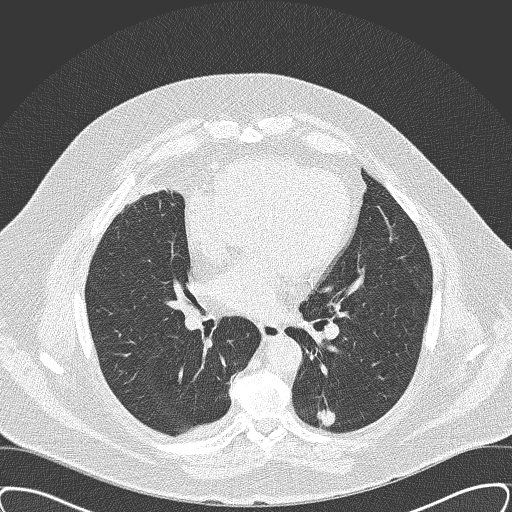
Low-dose screening chest CT, axial slice. Third screening round (two years after baseline). Lung window (W 1500 / L -600 HU). 2 mm slice thickness. Lung (sharp) reconstruction kernel (B50f). 120 kVp. Slice 87 of 161 in the series. 512 × 512 image matrix. Male, age 63 years at enrolment.
- Expert-annotated lung lesion, bounding box <301,393,354,444> (left, top, right, bottom; pixels).
- The screening reader recorded 2 non-calcified nodules or masses ≥4 mm on this exam; which of them this box marks is not recorded.
- Official screen result: positive, other.
- Participant outcome: lung cancer diagnosed 47 days after this screen — squamous cell carcinoma, NOS, left lower lobe, moderately differentiated (G2), stage IA (AJCC 6th edition), 15 mm at pathology.